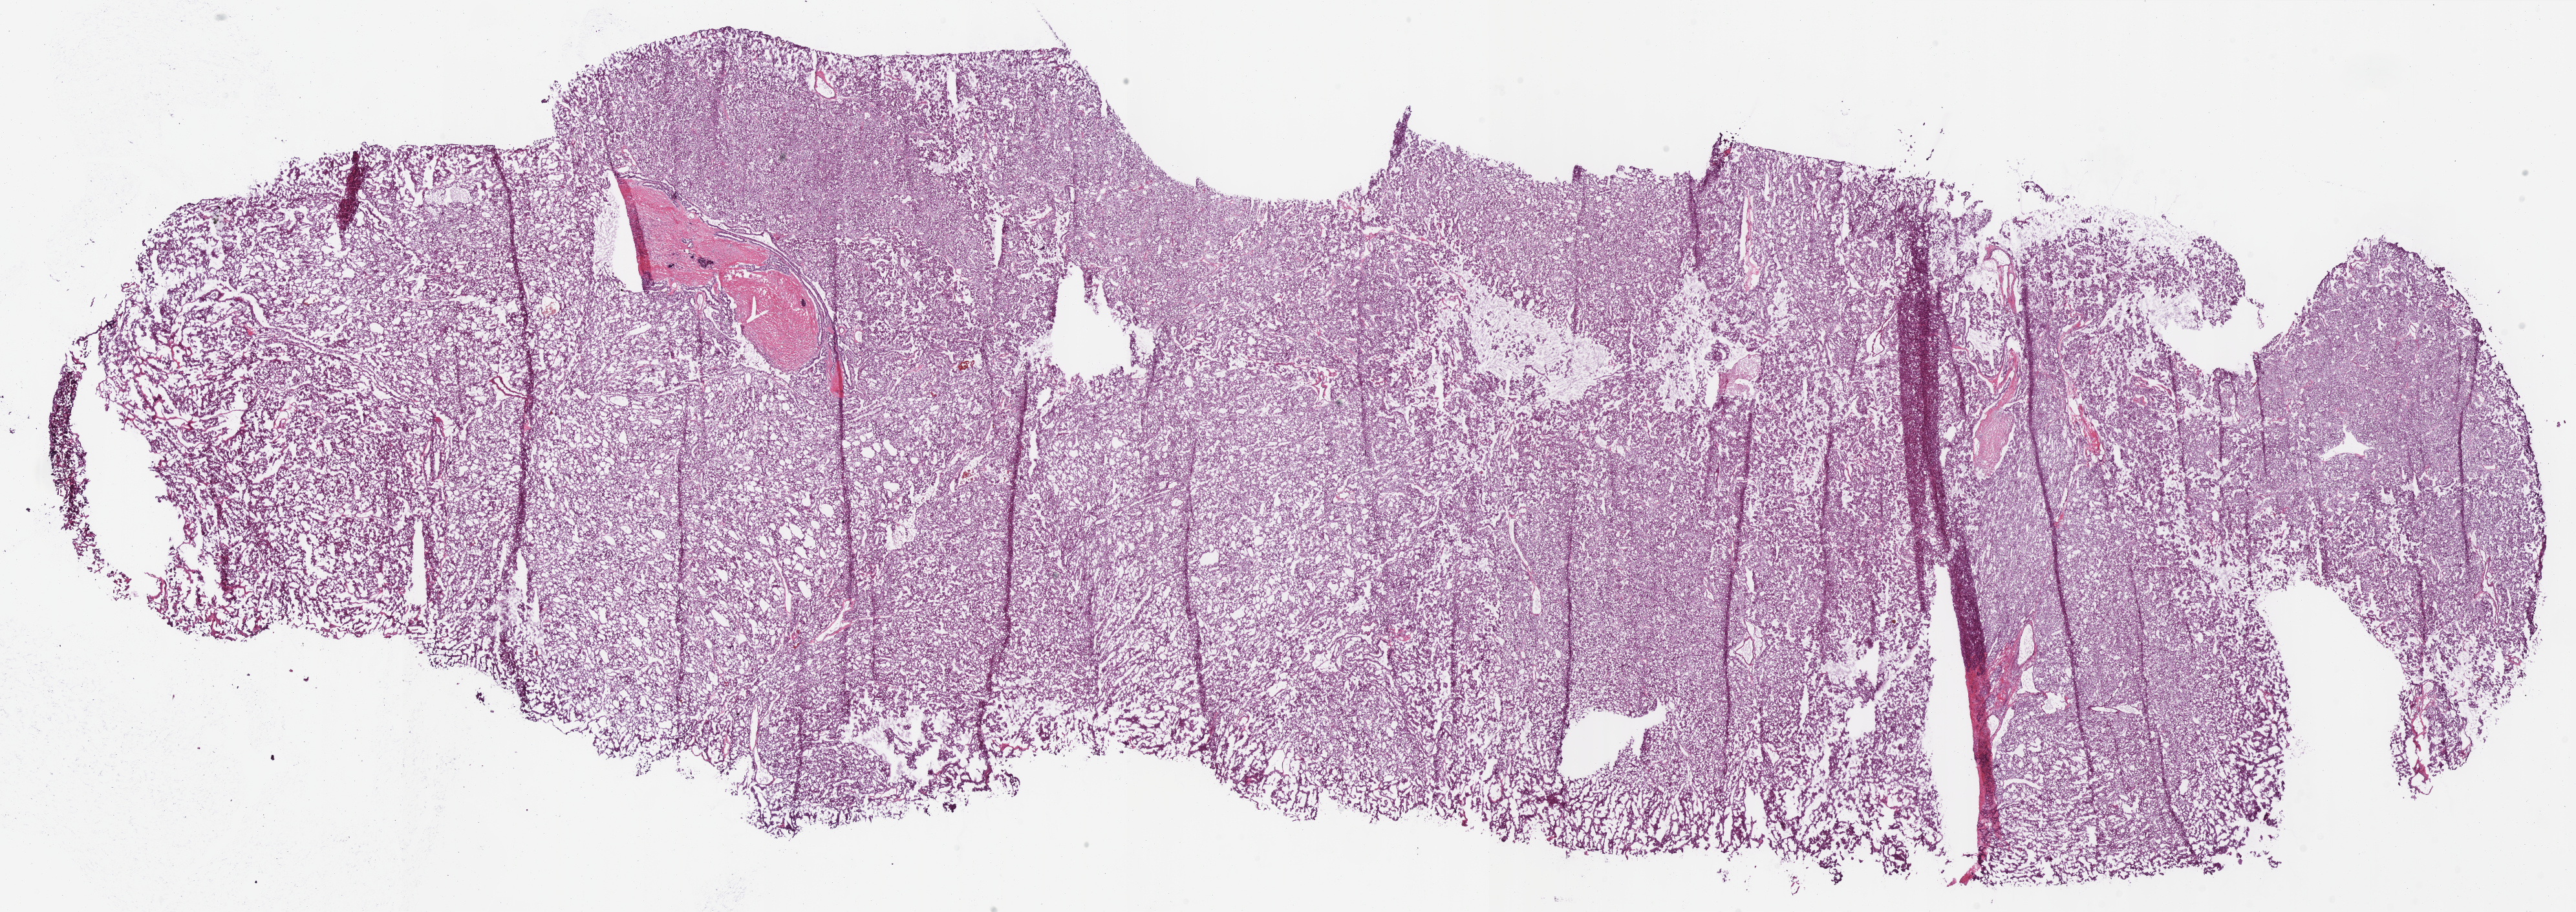
H&E whole-slide image — whole scanned area (about 31.3 x 11.1 mm, from a 40x scan) shown as a low-resolution overview, frozen section, sample: primary tumour, kidney. Female, age 30 years at initial diagnosis. Composition of this section per pathologist review: tumour cells 90%, tumour nuclei 90%, normal cells 0%, stromal cells 10%, necrosis 0%.
Histologic diagnosis: Renal cell carcinoma, chromophobe type. AJCC pathologic stage: I.